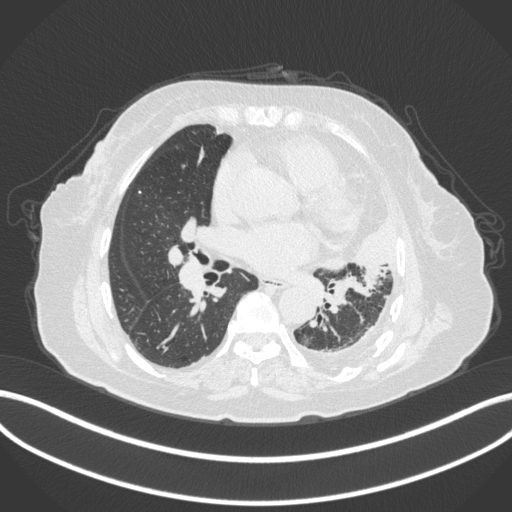
Chest CT, one axial slice. Slice 180 of 399 in the series (ordered by position). 120 kVp. Lung window (W 1500 / L -600 HU). 1 mm slice thickness. 512 × 512 image matrix, field of view 400 × 400 mm. Patient: female, 75 years. From the clinical record (not read from this slice): clinical TNM (as recorded): T3 N3 M1.
Structures marked on this image (bounding box drawn by a radiologist):
- lung tumour (recorded histology: adenocarcinoma): bounding box [x1, y1, x2, y2] px = [324, 223, 401, 279]